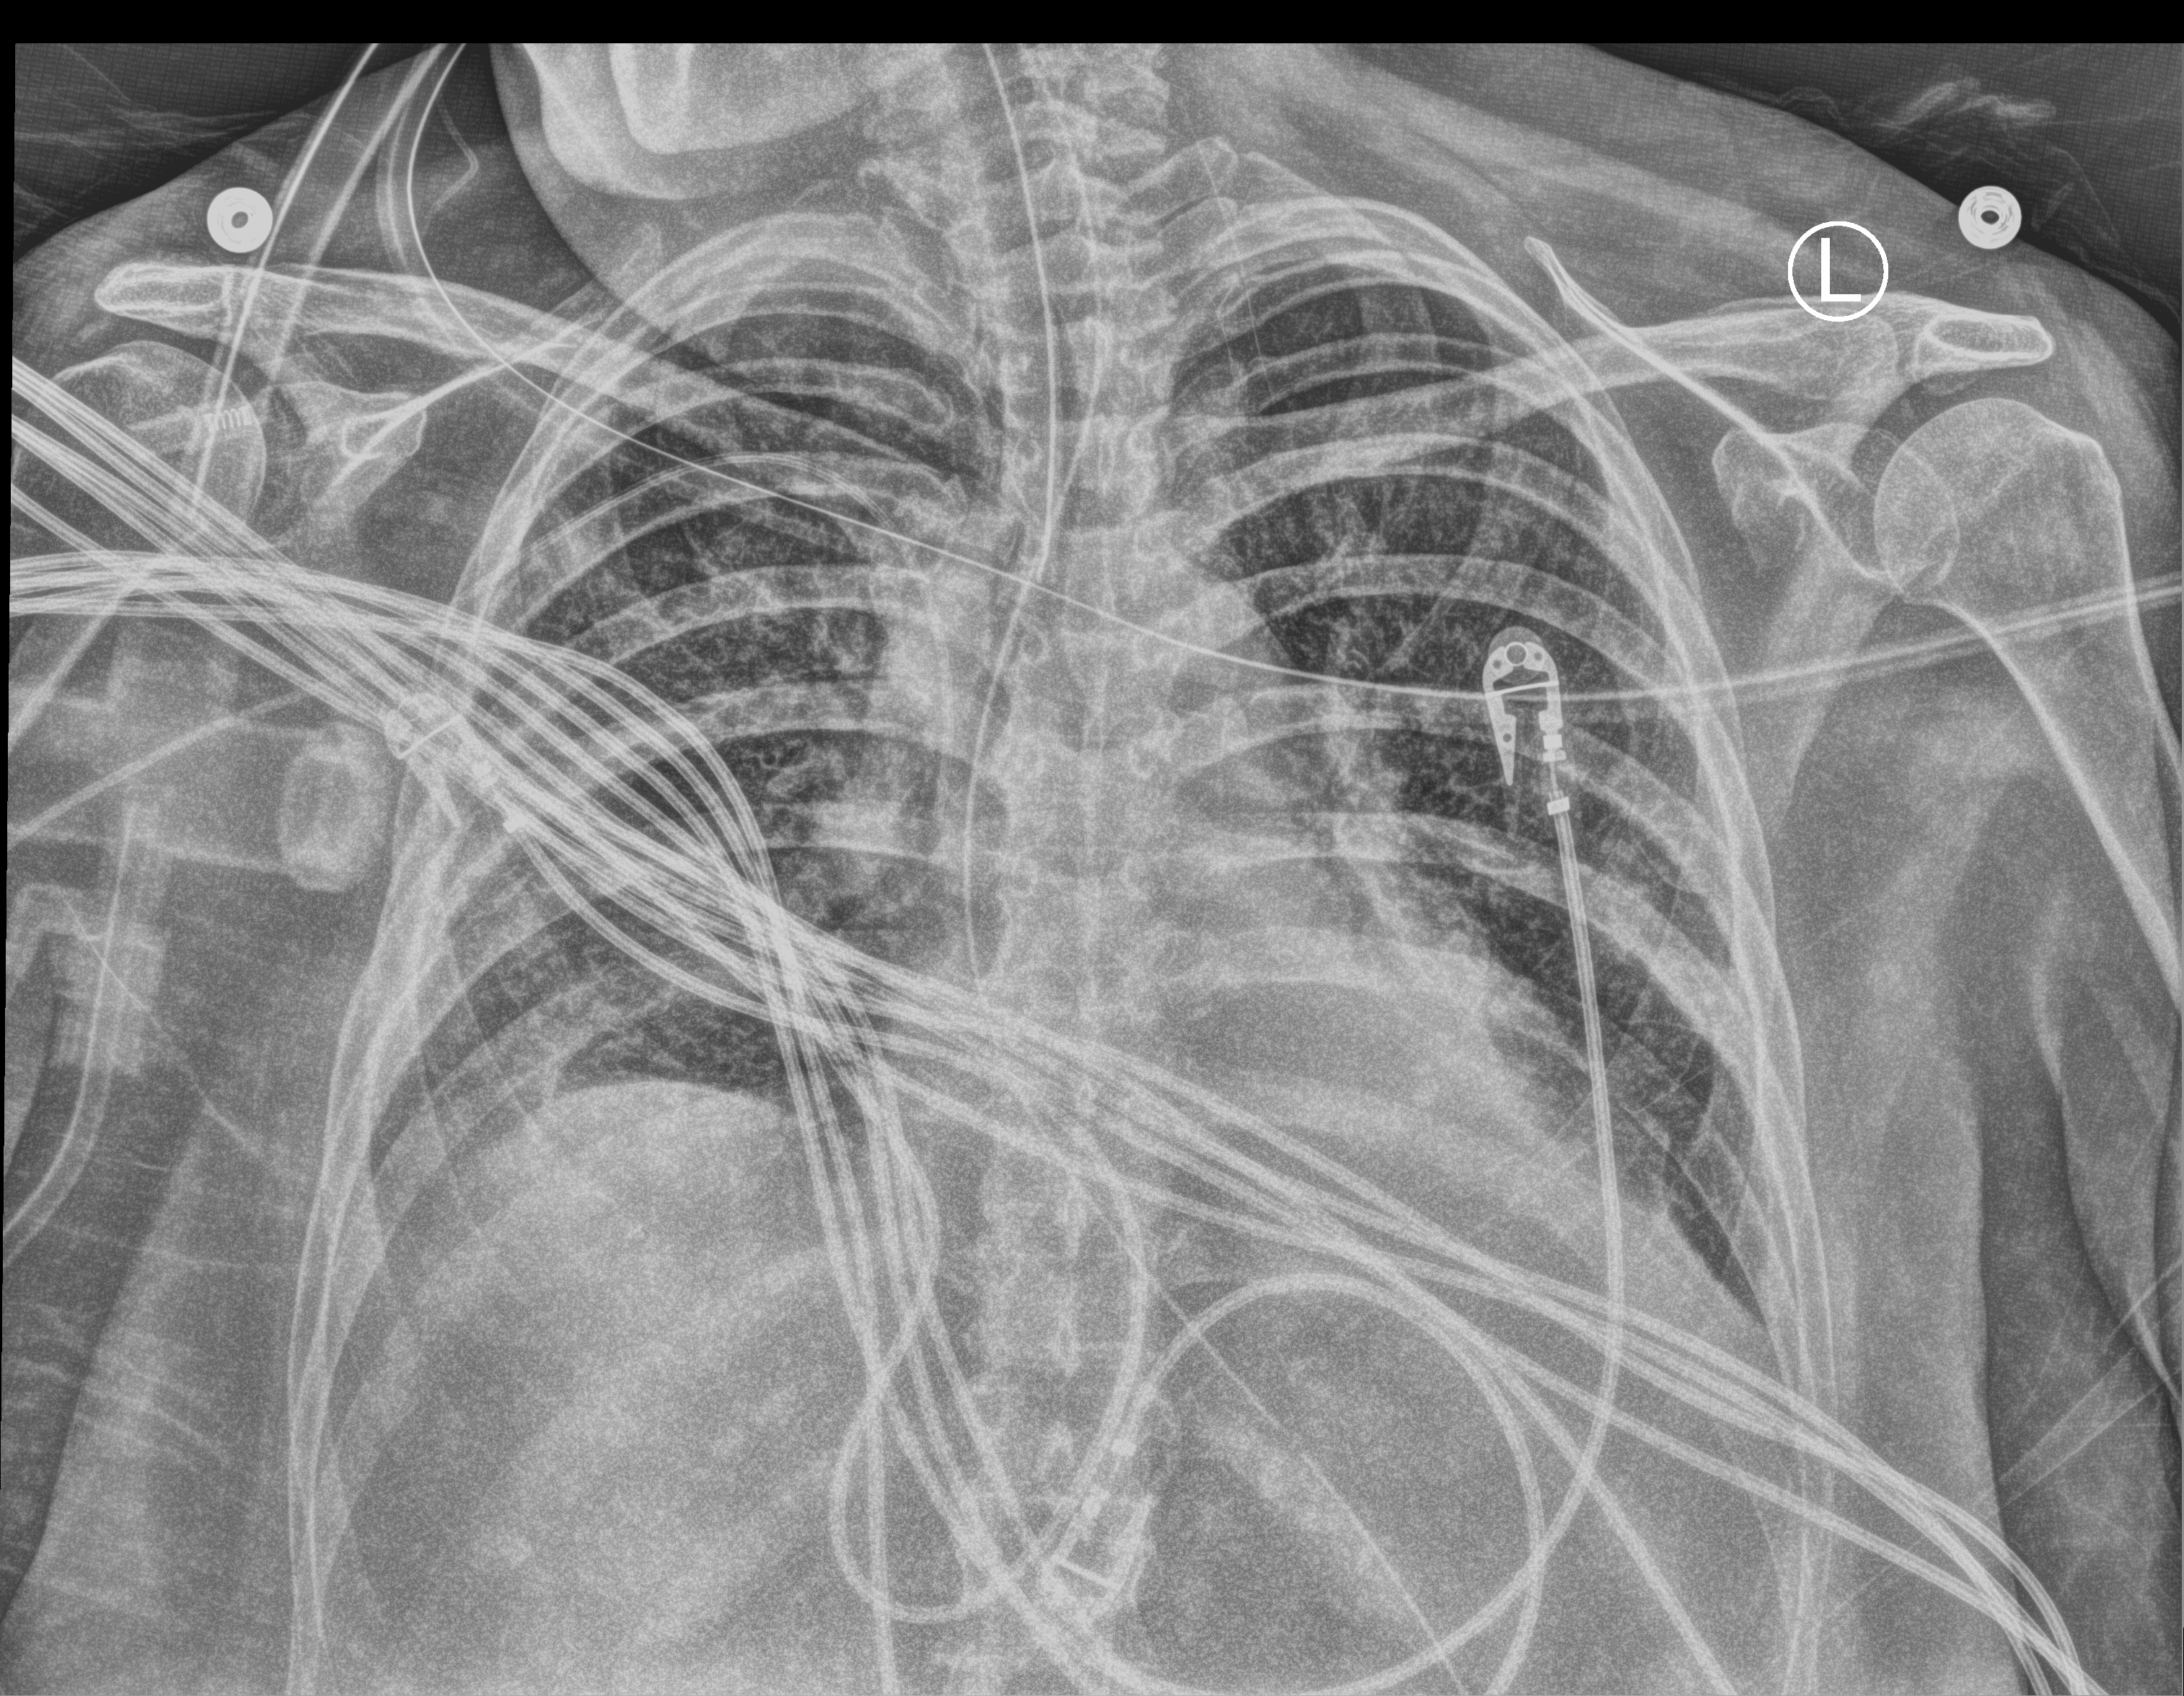
Chest X-ray (portable), anteroposterior (AP) projection. Patient hospitalised with COVID-19; female, aged 60–74 years.
Admission-level facts for this patient (not findings on this image; timing relative to this image not recorded): admitted to intensive care during this hospital stay: yes; mechanically ventilated during this hospital stay: yes.